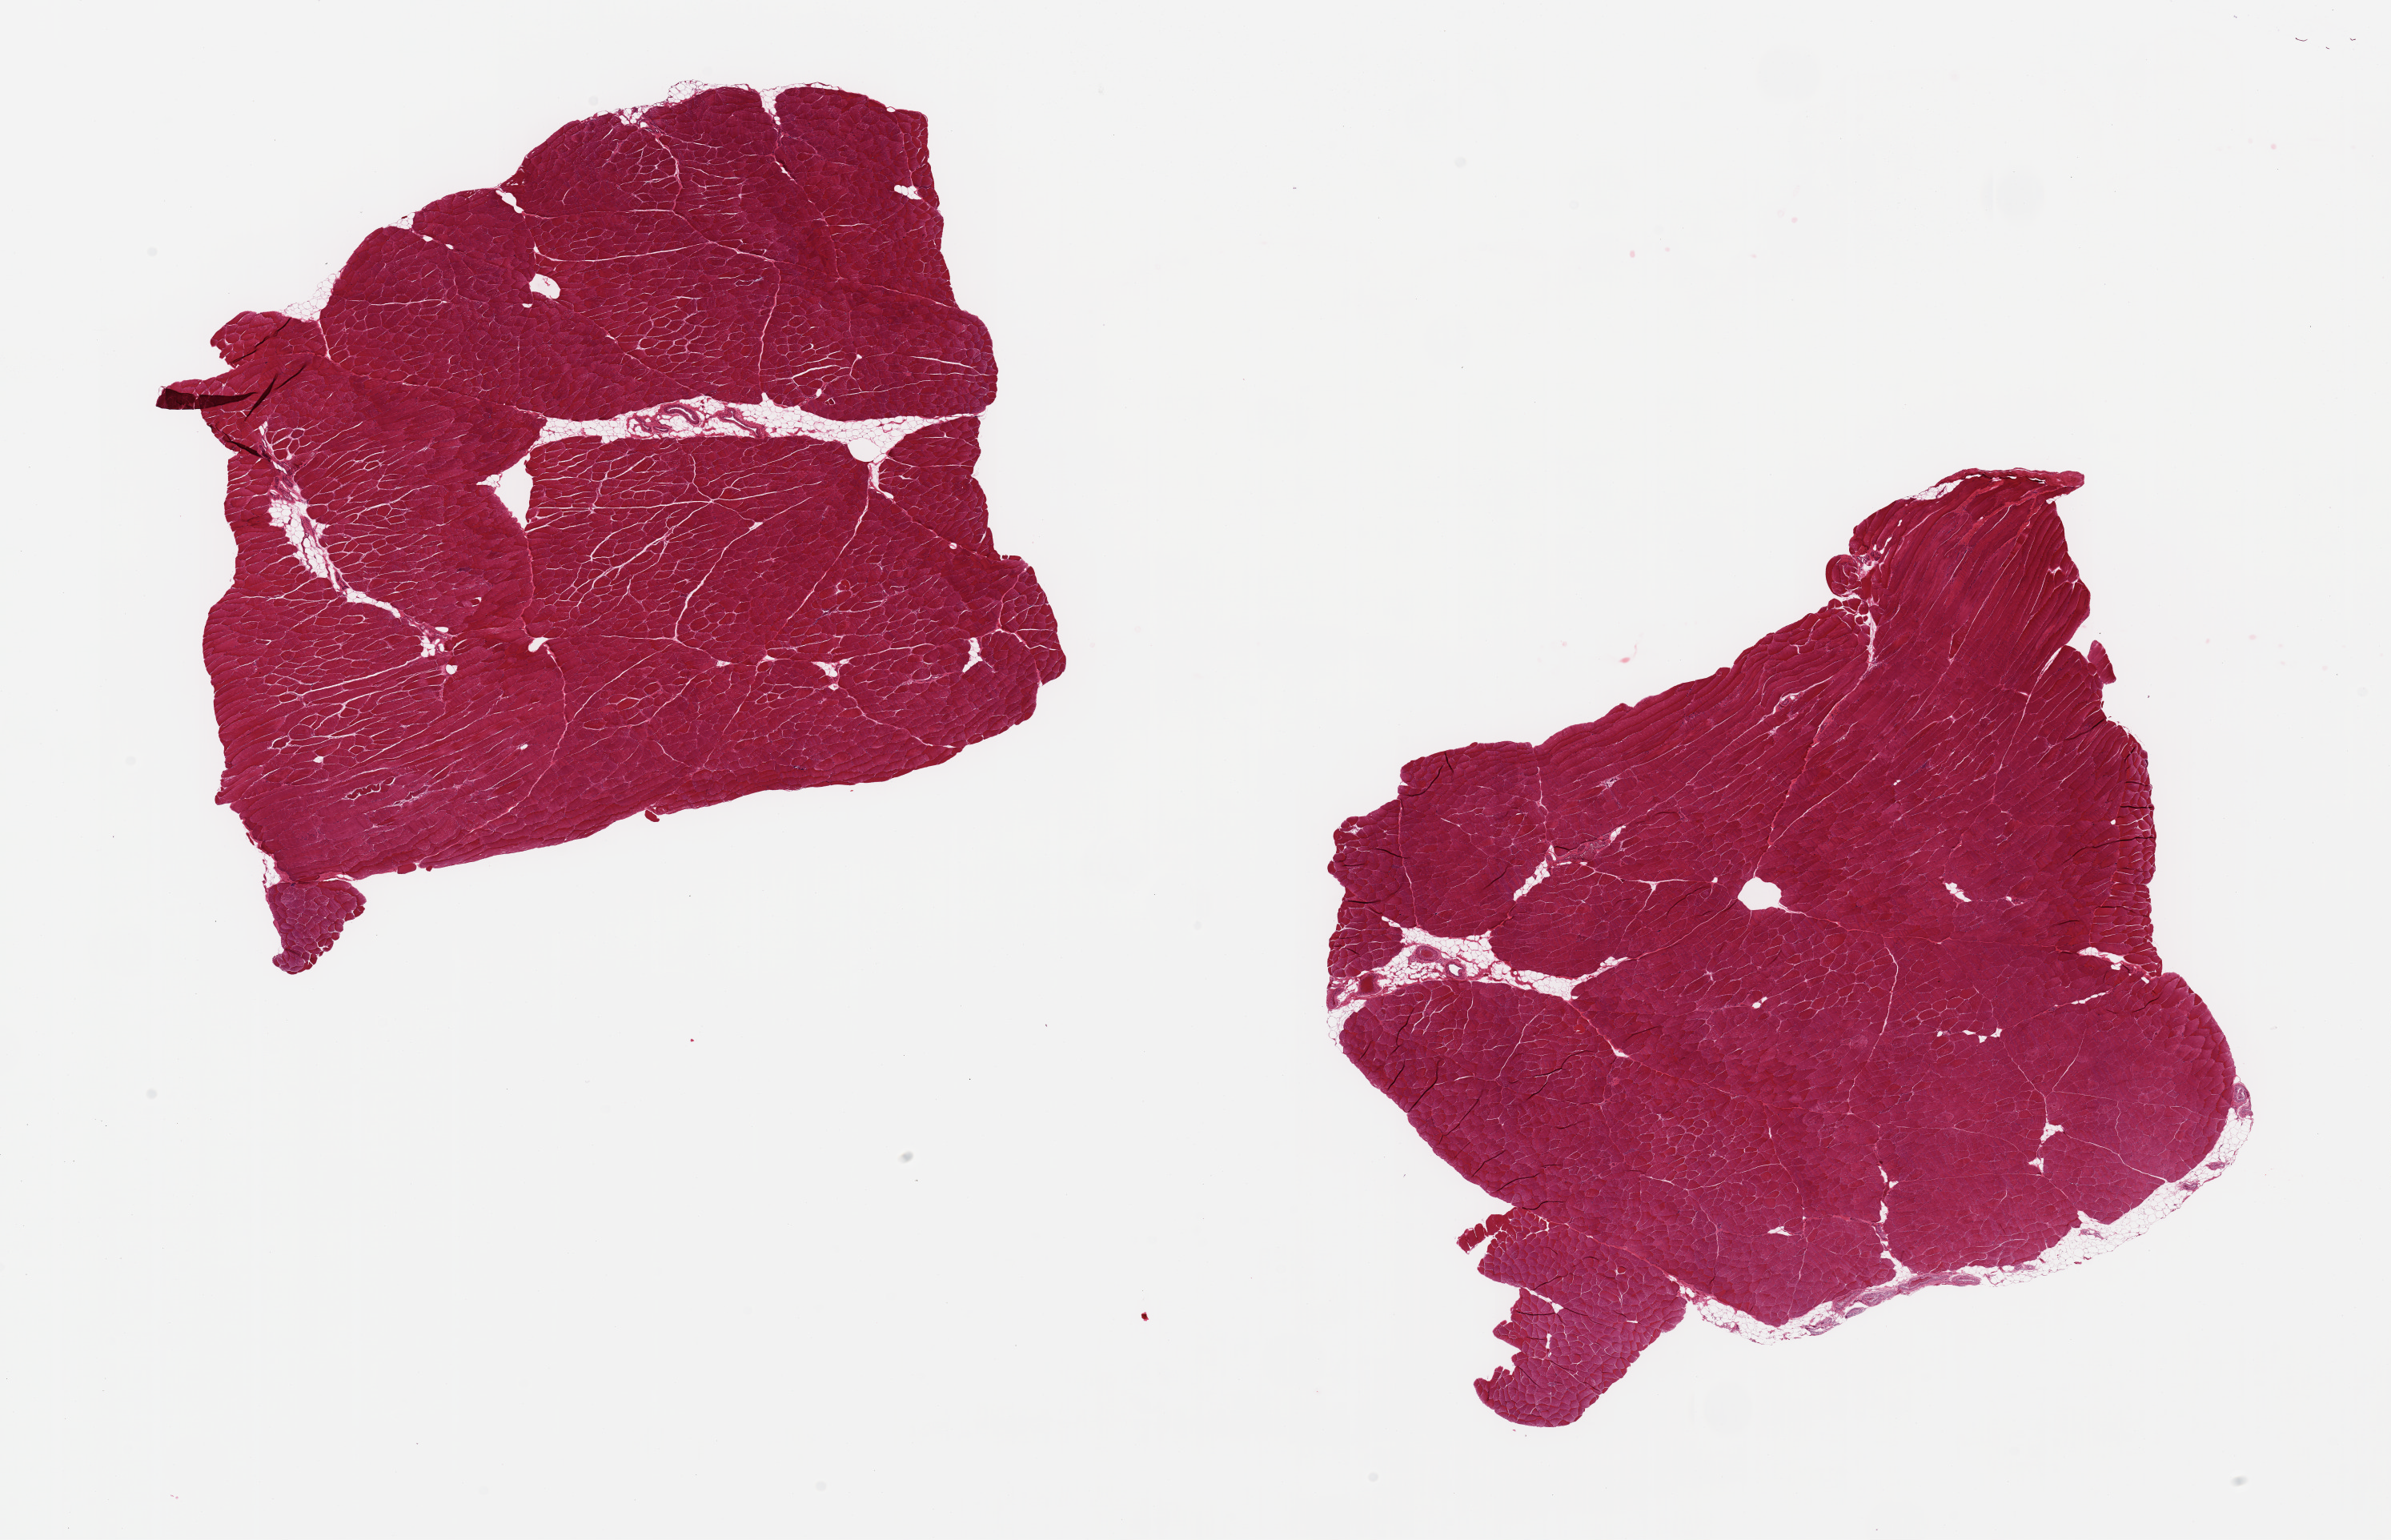
Hematoxylin and eosin (H&E) whole-slide image, brightfield — low-resolution overview of the scanned area, about 23.6 x 15.2 mm, PAXgene-fixed paraffin-embedded (PFPE) section, sampled site (target tissue): skeletal muscle, donor tissue sample.
Reviewer comment on this tissue sample: 2 pieces, minimal interstitial fat.